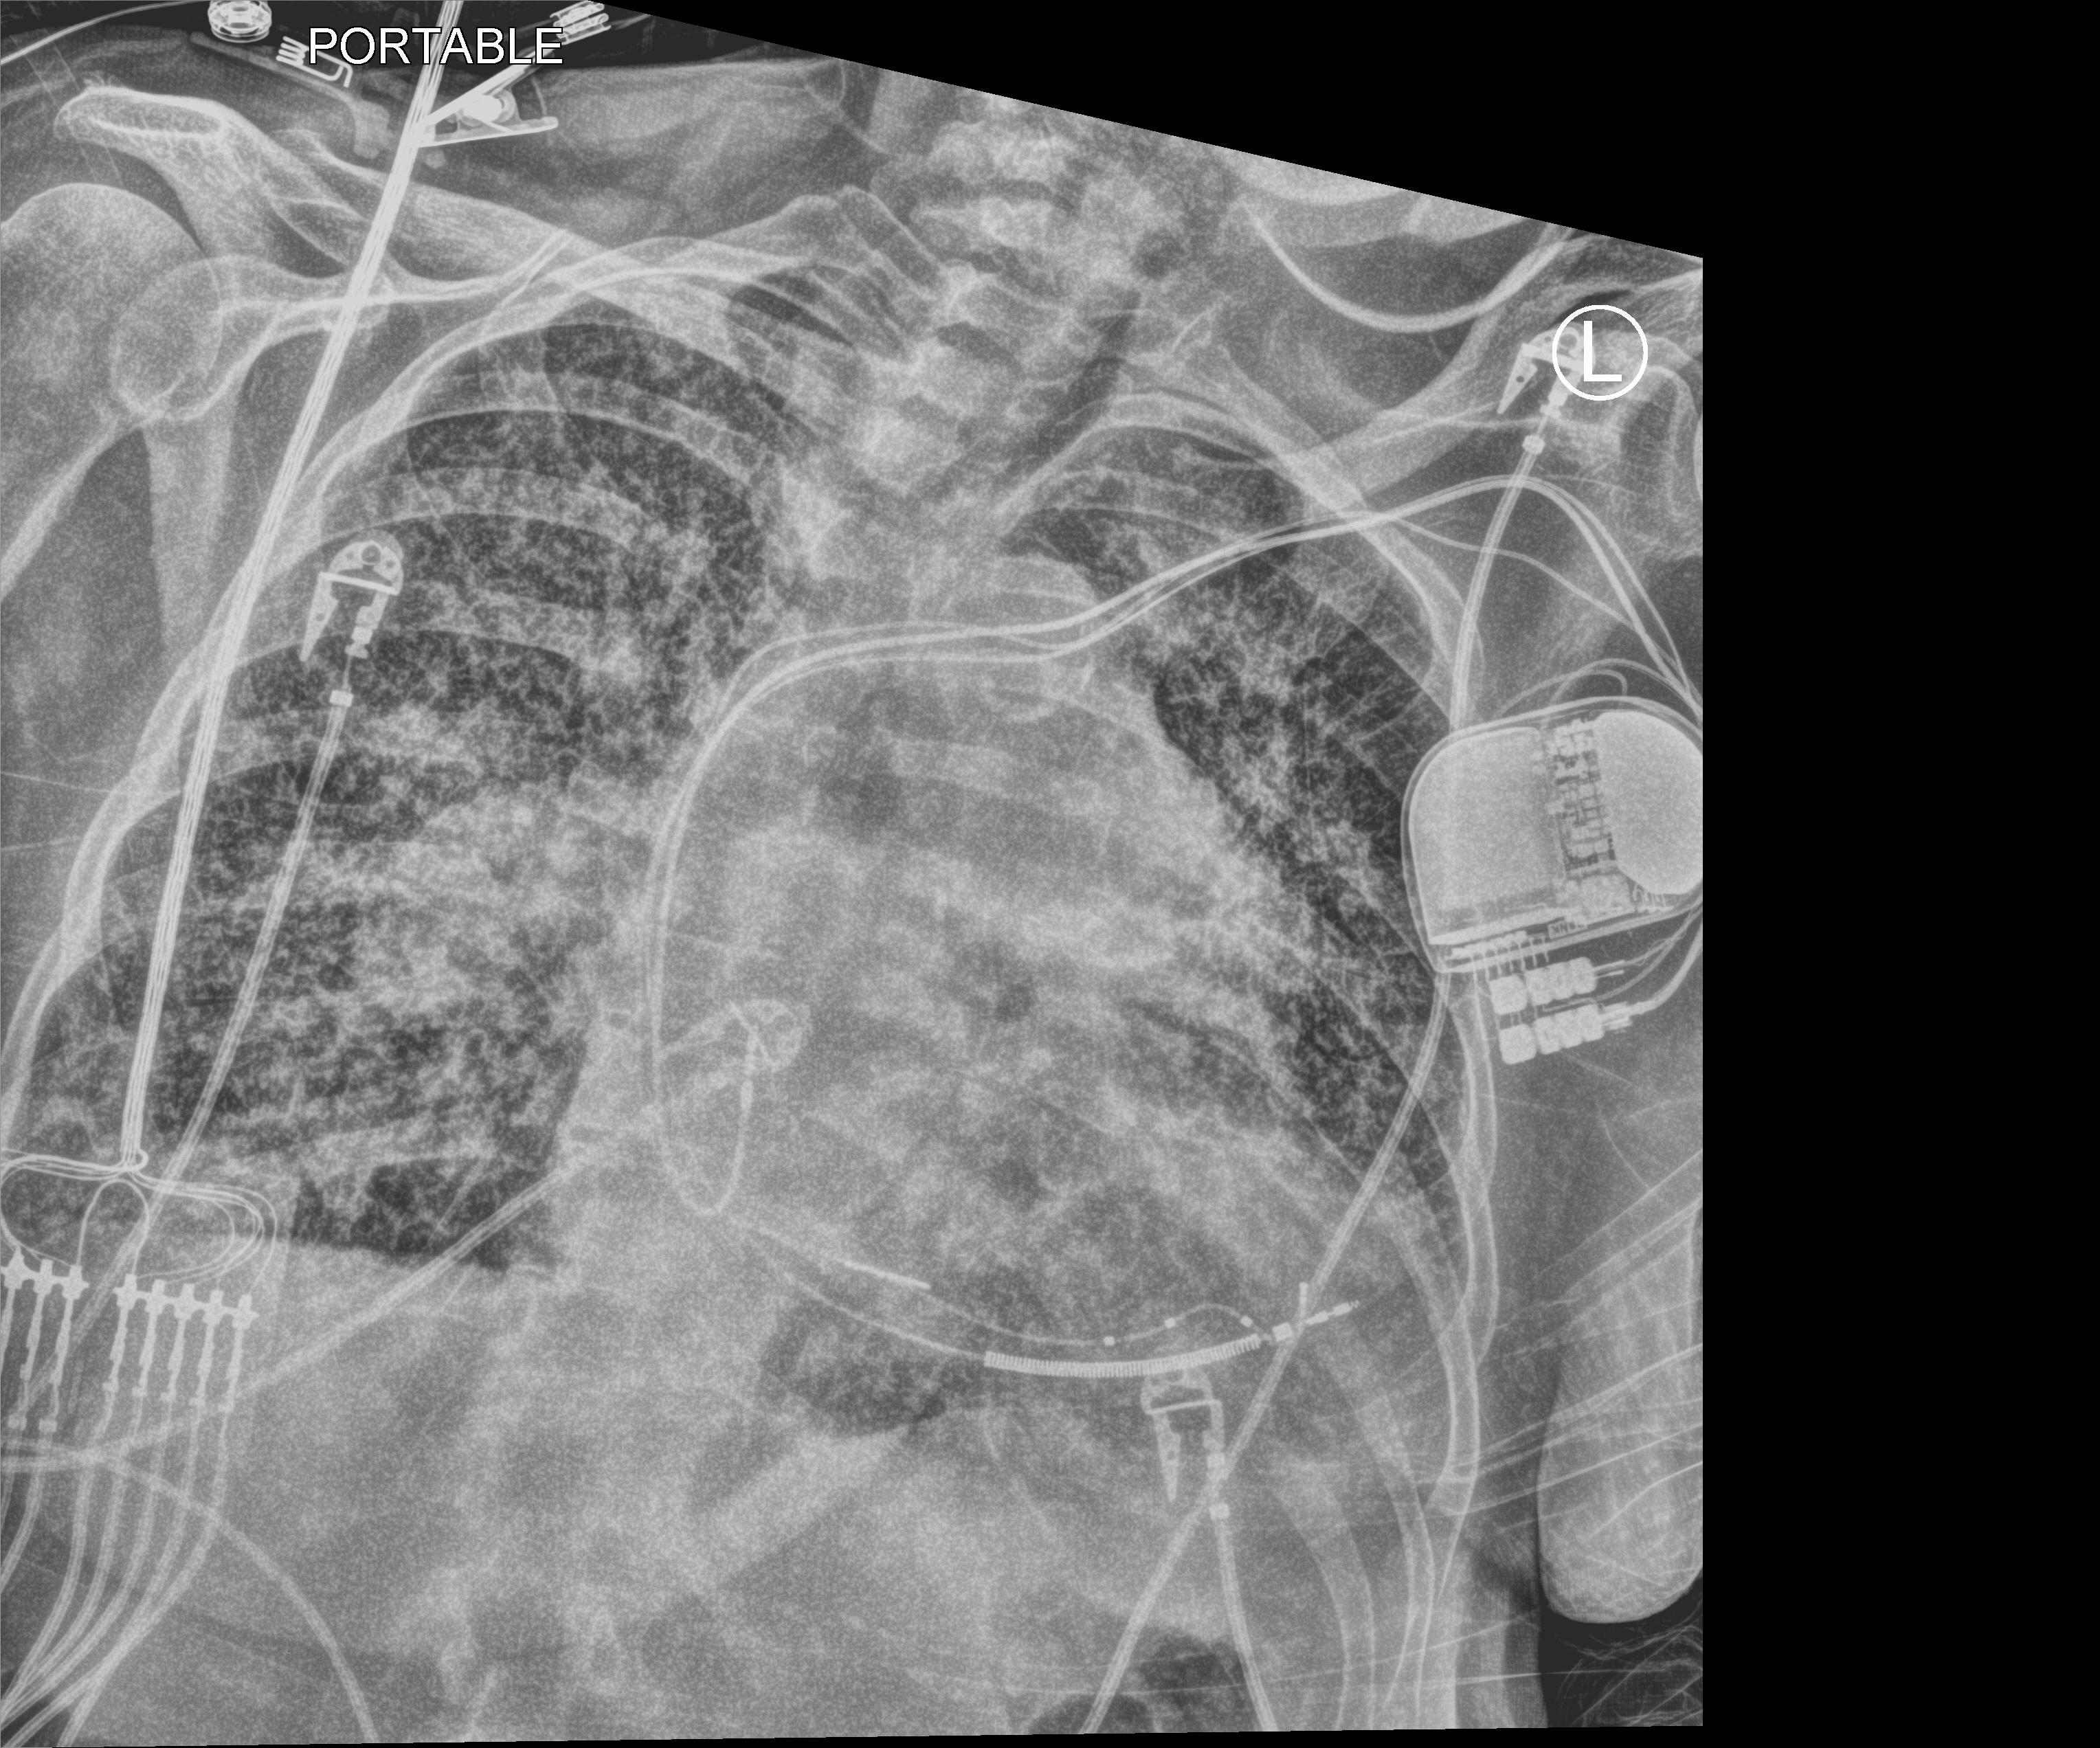
Chest X-ray (portable); anteroposterior (AP) projection. Patient hospitalised with COVID-19; female, aged 60–74 years.
Admission-level facts for this patient (not findings on this image; timing relative to this image not recorded):
- mechanically ventilated during this hospital stay: no
- admitted to intensive care during this hospital stay: yes